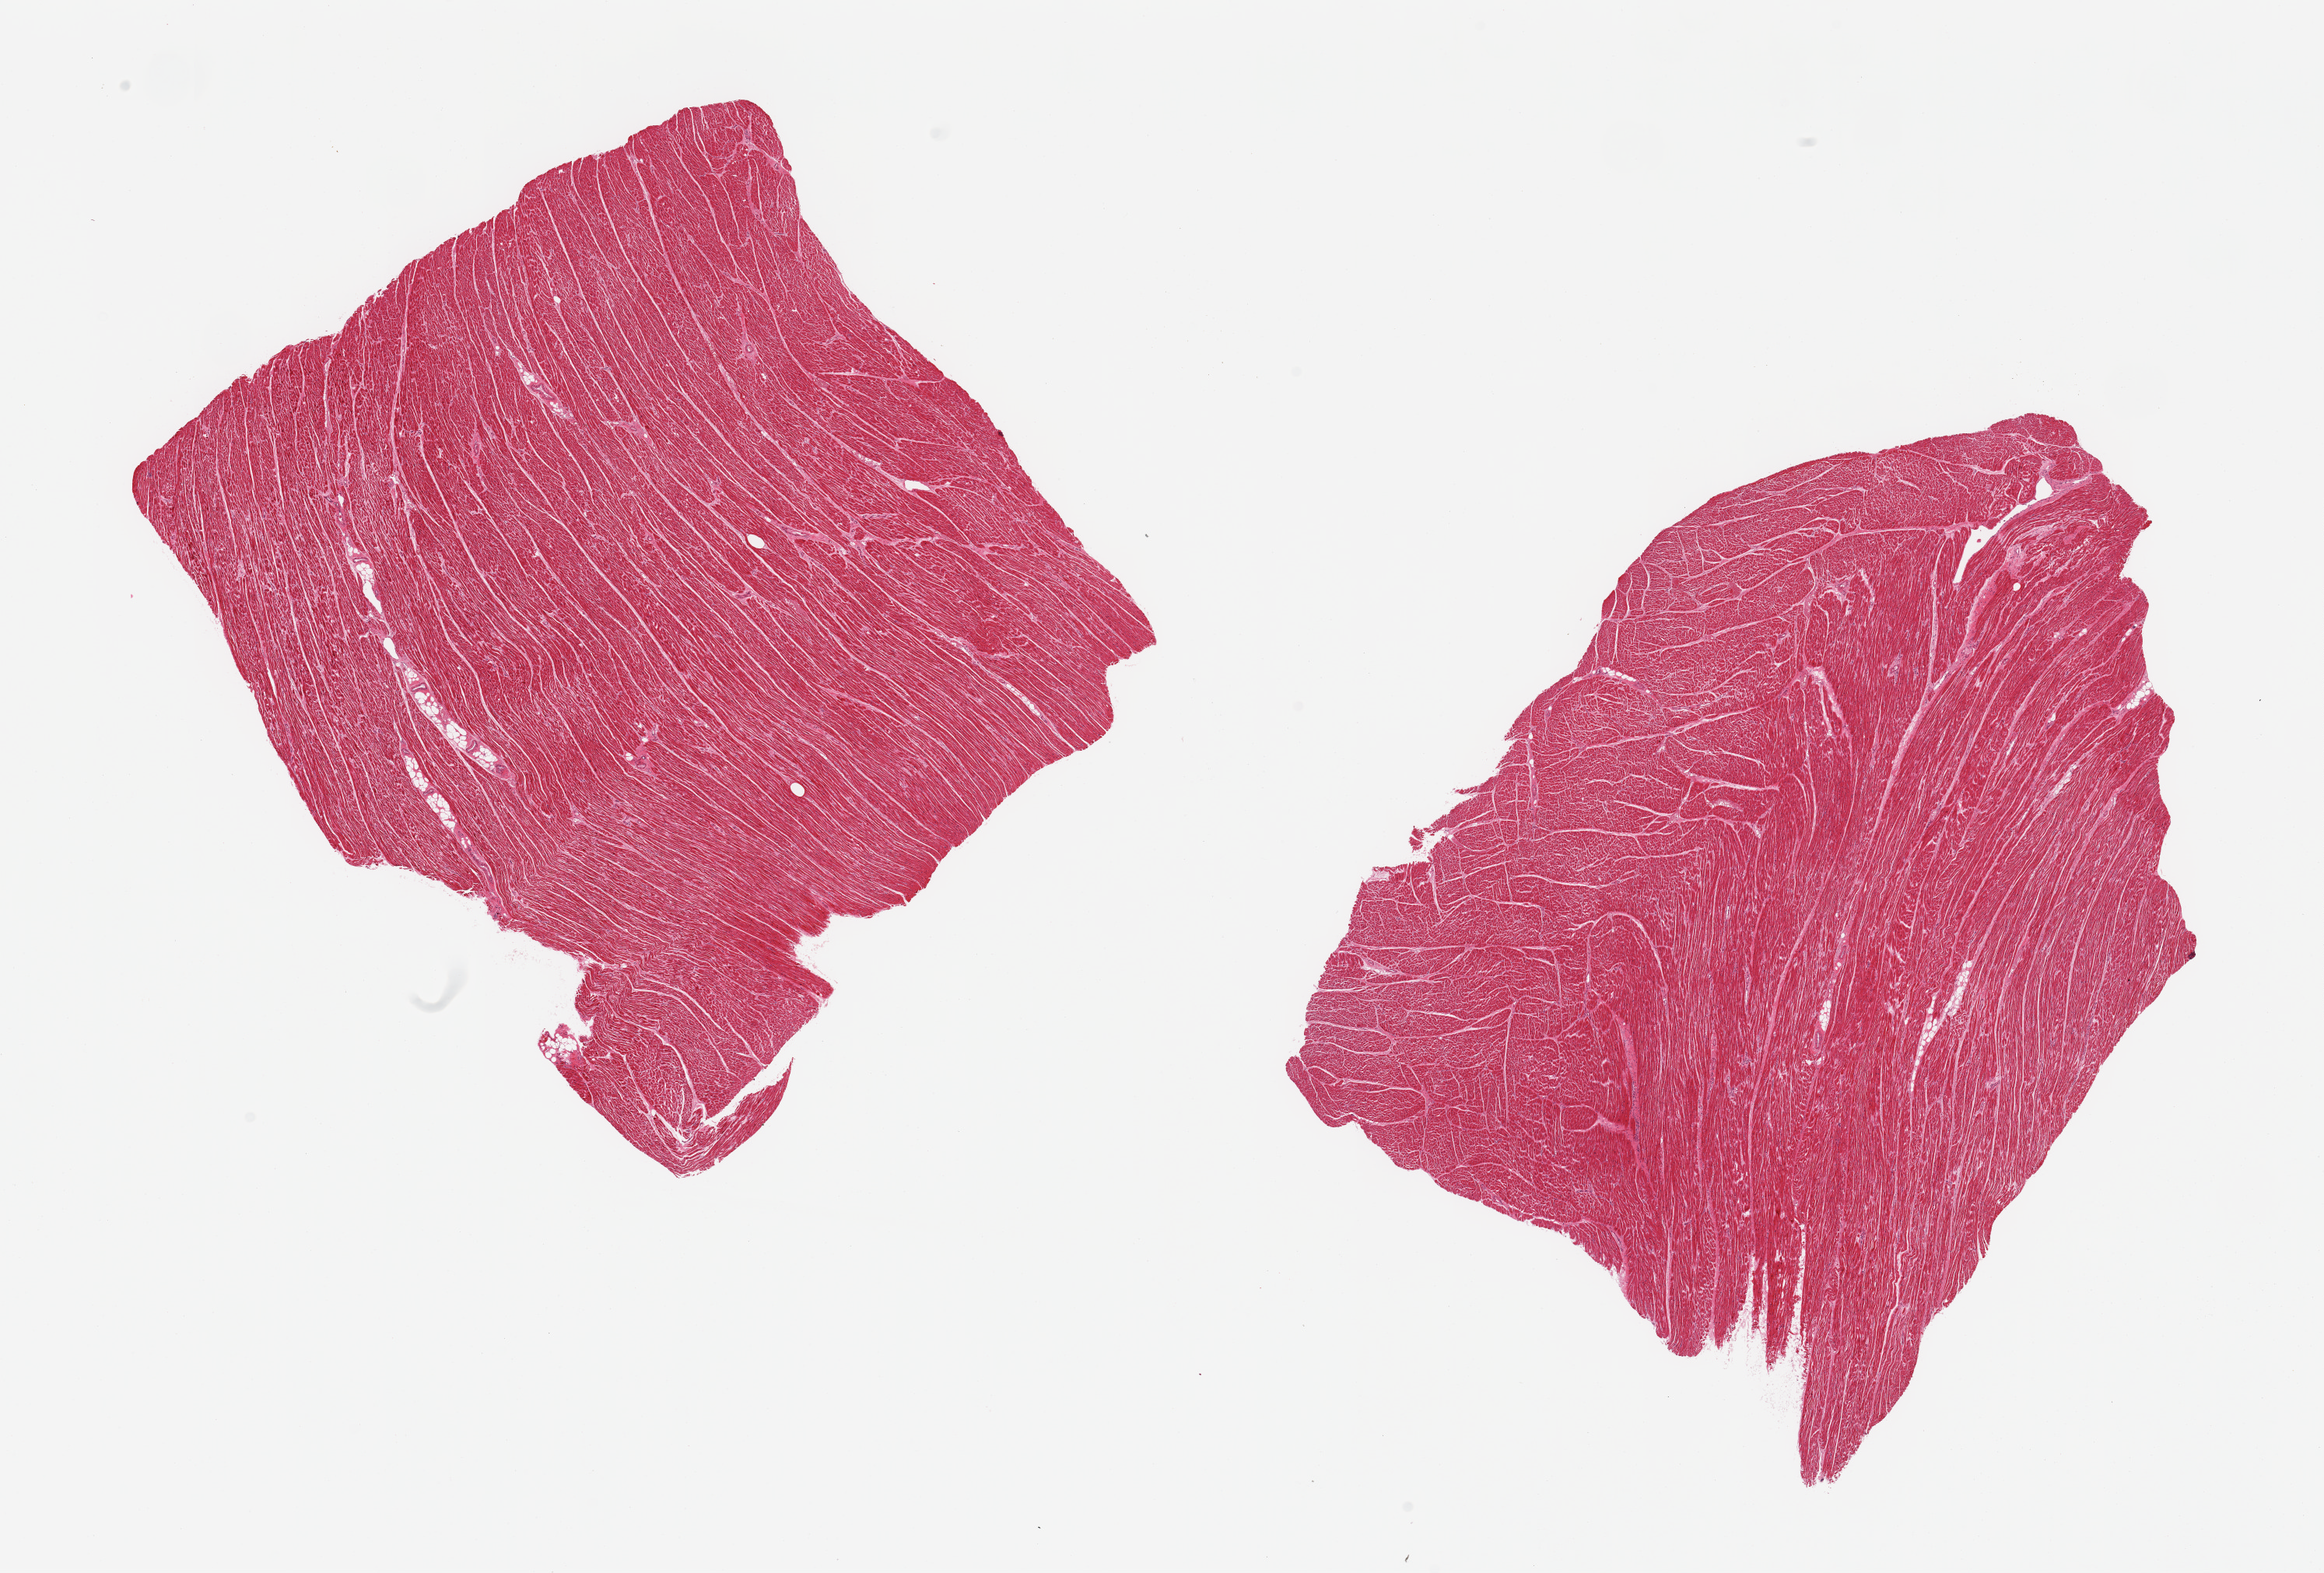
Whole-slide image, haematoxylin and eosin stain — low-resolution overview of the scanned area, about 23.6 x 16.0 mm (from a 20x scan); PAXgene-fixed, paraffin-embedded tissue; sampled site (target tissue): heart; donor tissue sample. Male donor.
Pathologist's review note for this sample: 2 pieces.